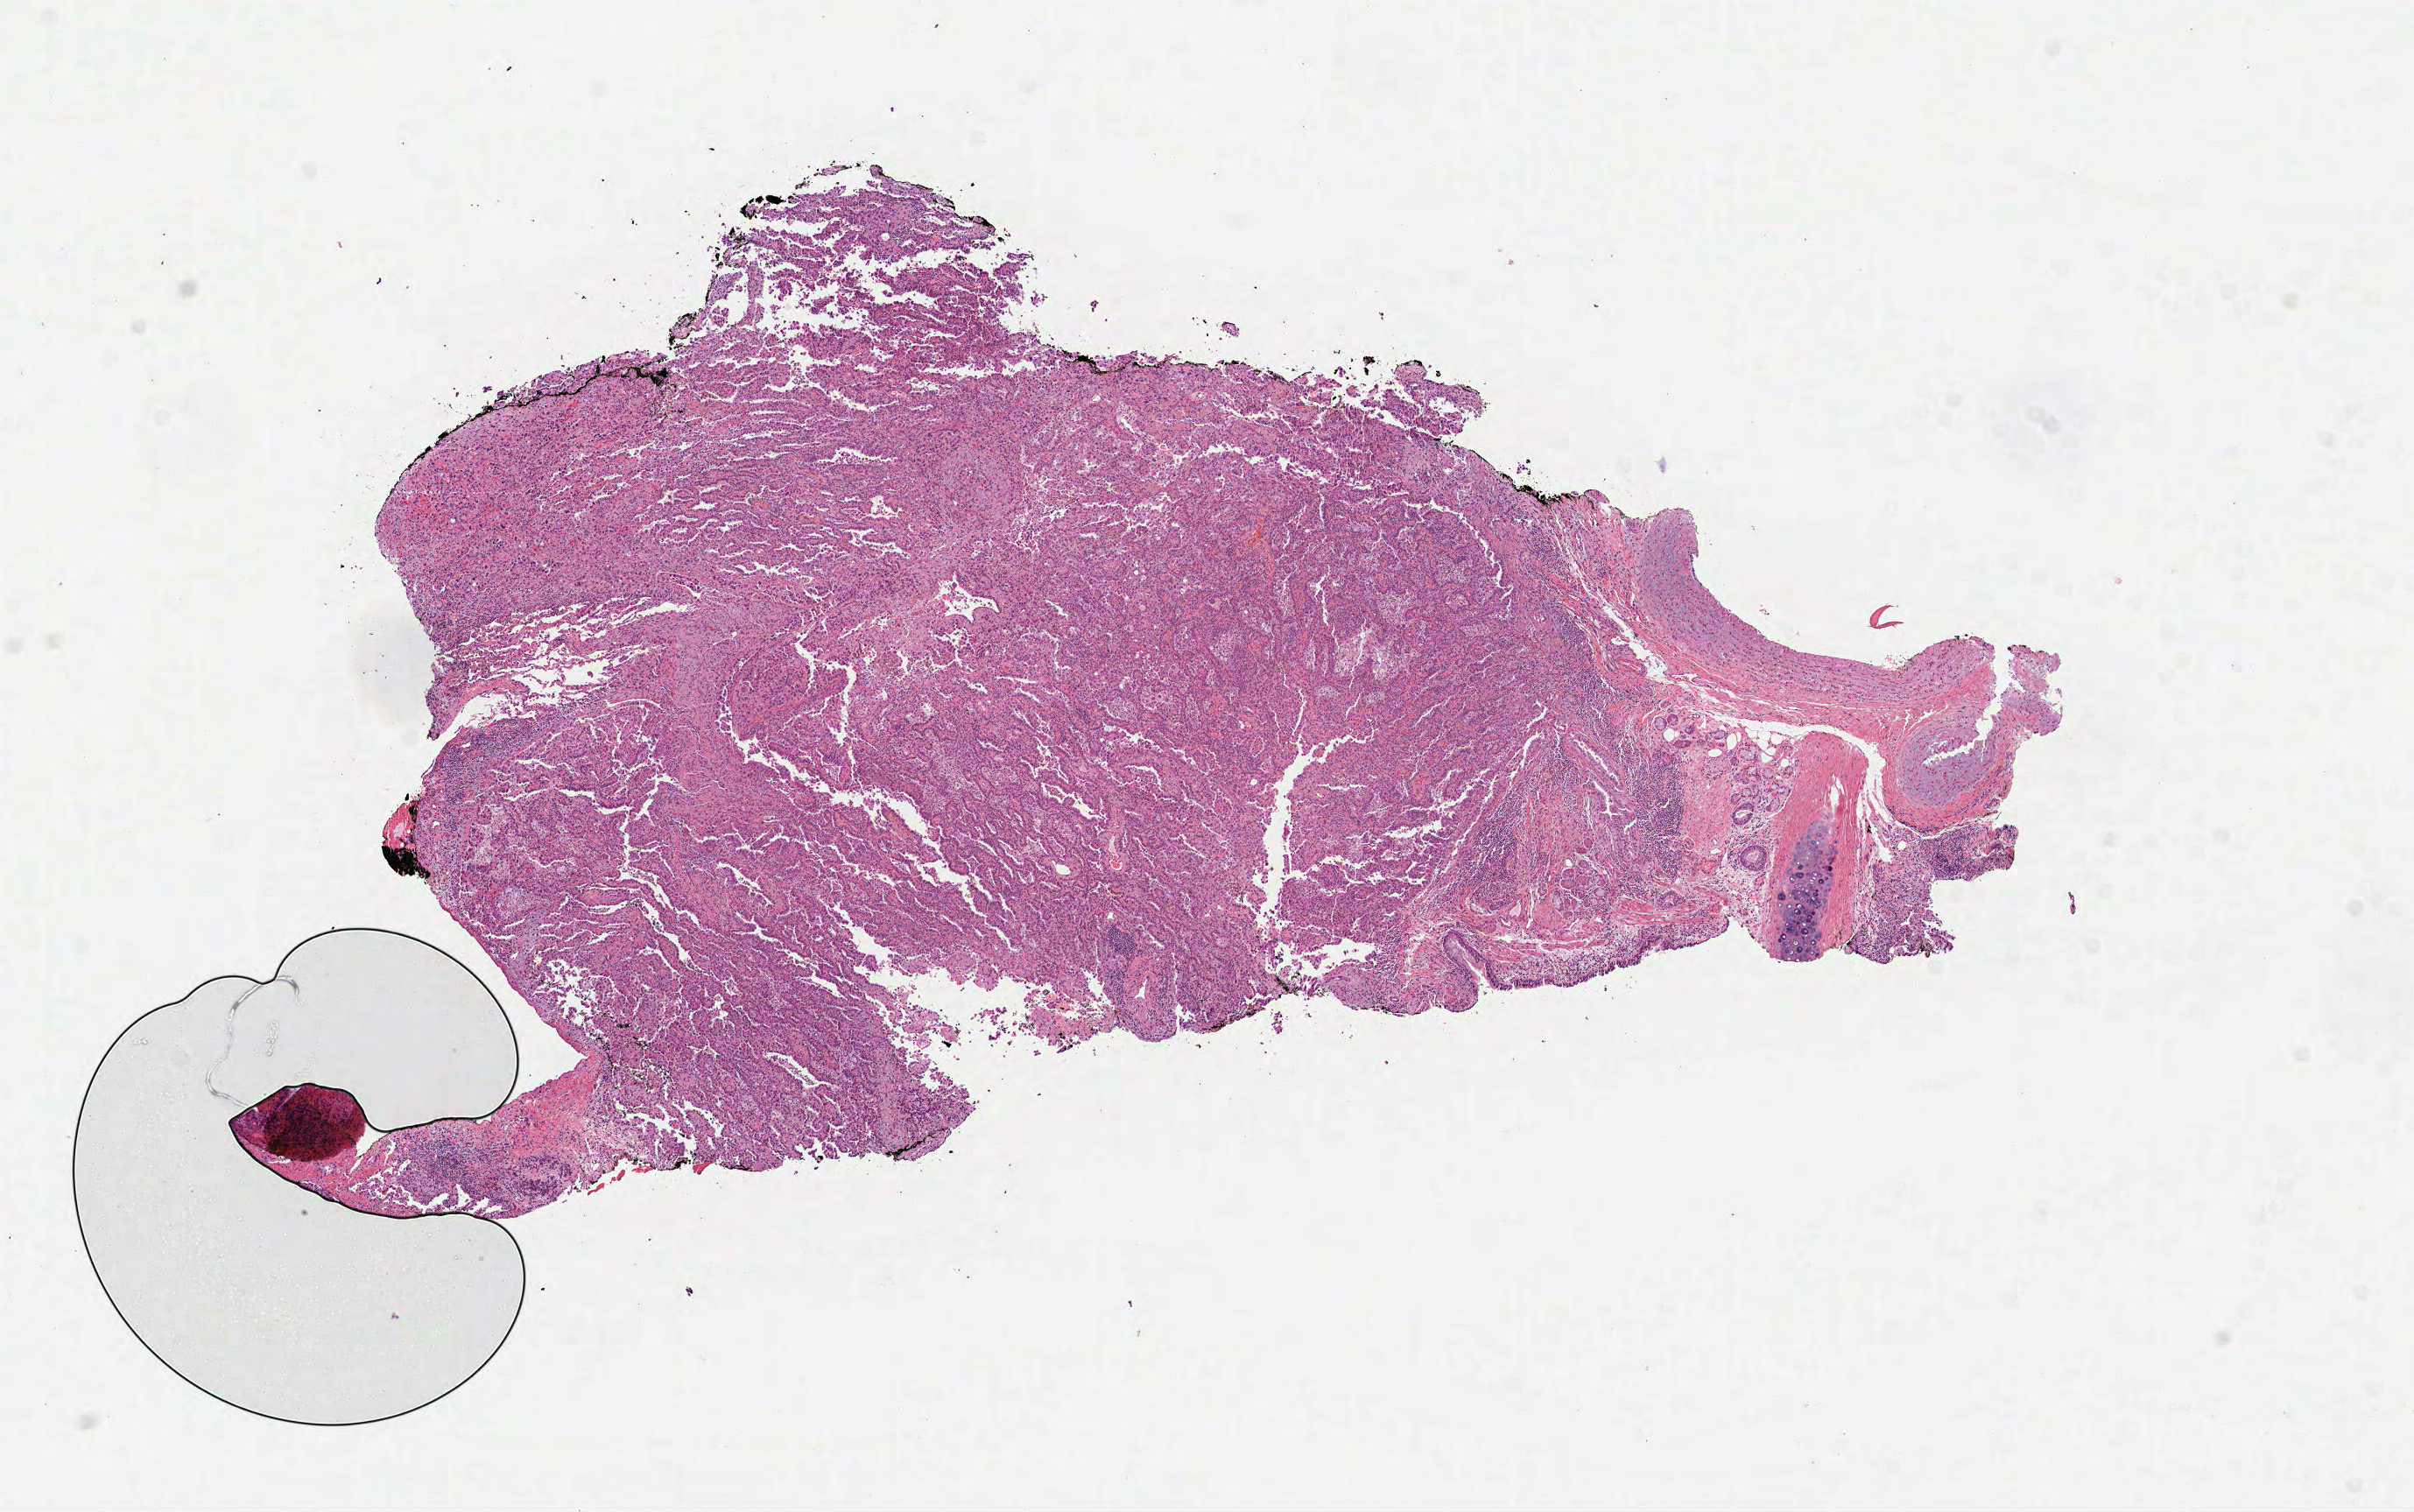
H&E-stained whole-slide image — low-resolution overview of the scanned area, about 11.1 x 7.0 mm; formalin-fixed paraffin-embedded (FFPE) diagnostic section; primary tumour sample from the lung. Female patient; age at initial diagnosis 70 years.
Histologic diagnosis: Adenocarcinoma, NOS (middle lobe, lung). AJCC pathologic stage: IA (7th edition).